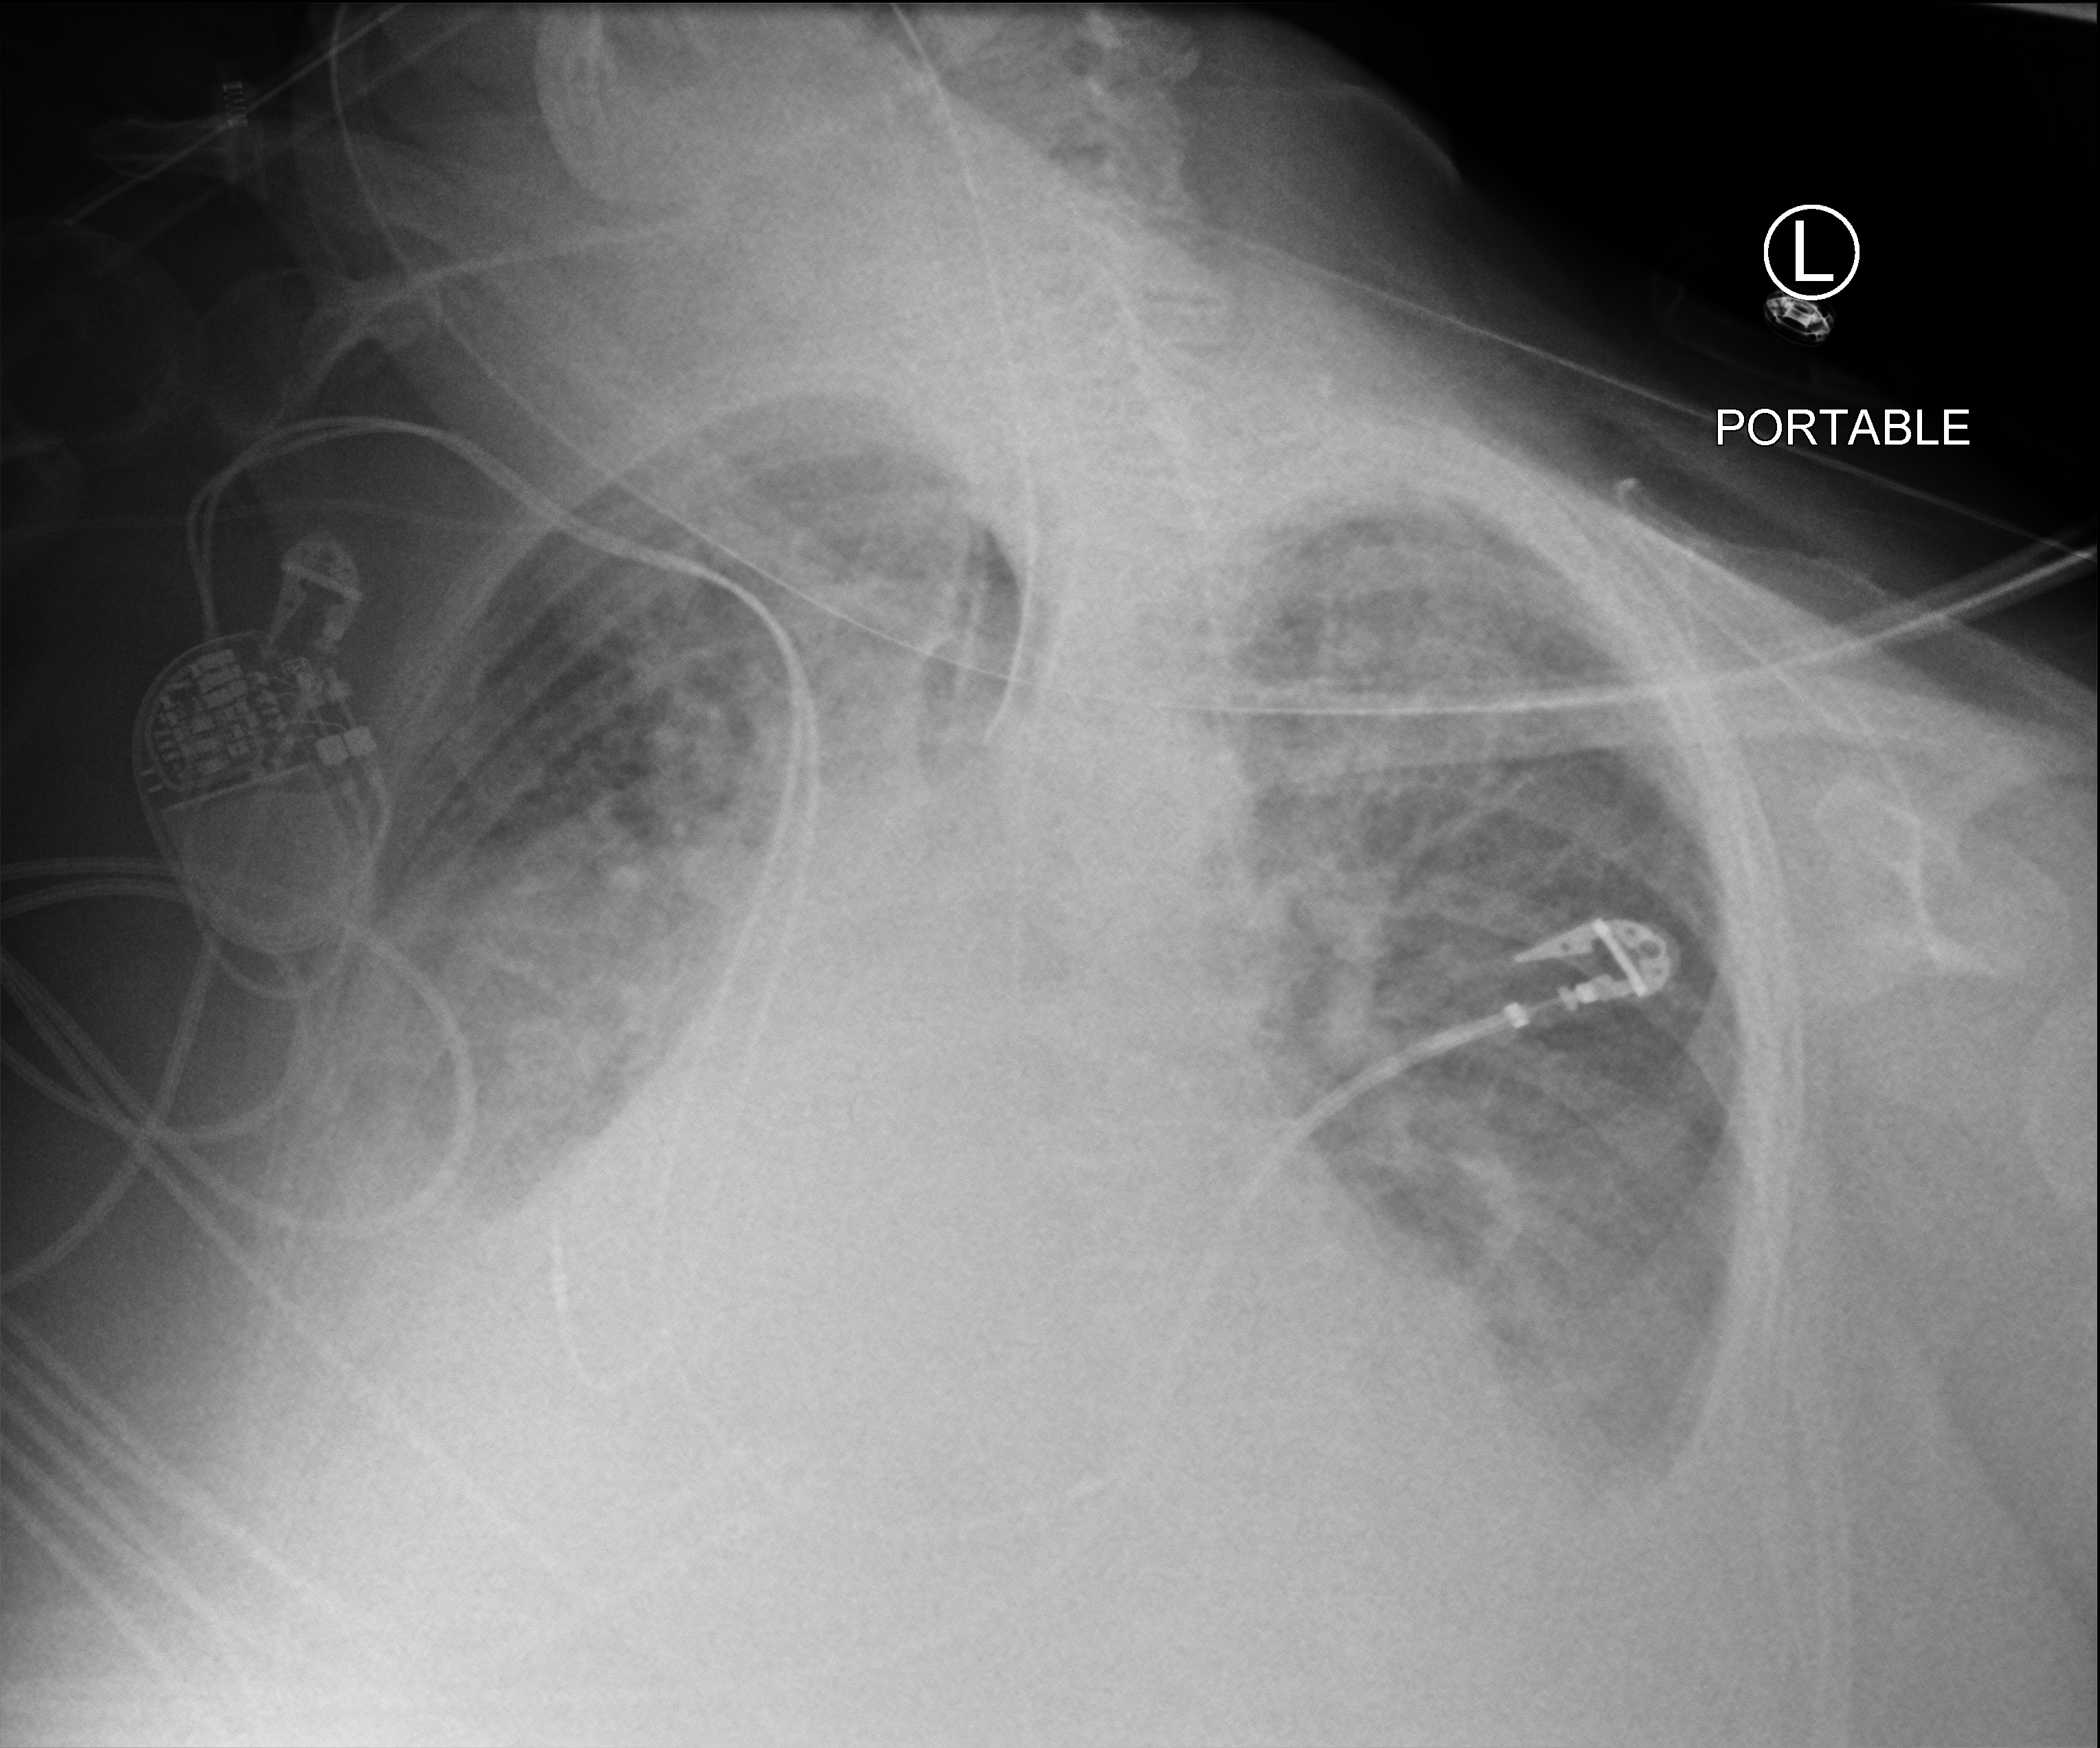
Bedside chest radiograph (computed radiography), anteroposterior (AP) projection. Female patient hospitalised with COVID-19, age 75–90 years.
From the hospital-stay record, not from the radiograph (when in the stay this image was taken is not recorded):
- admitted to intensive care during this hospital stay: yes